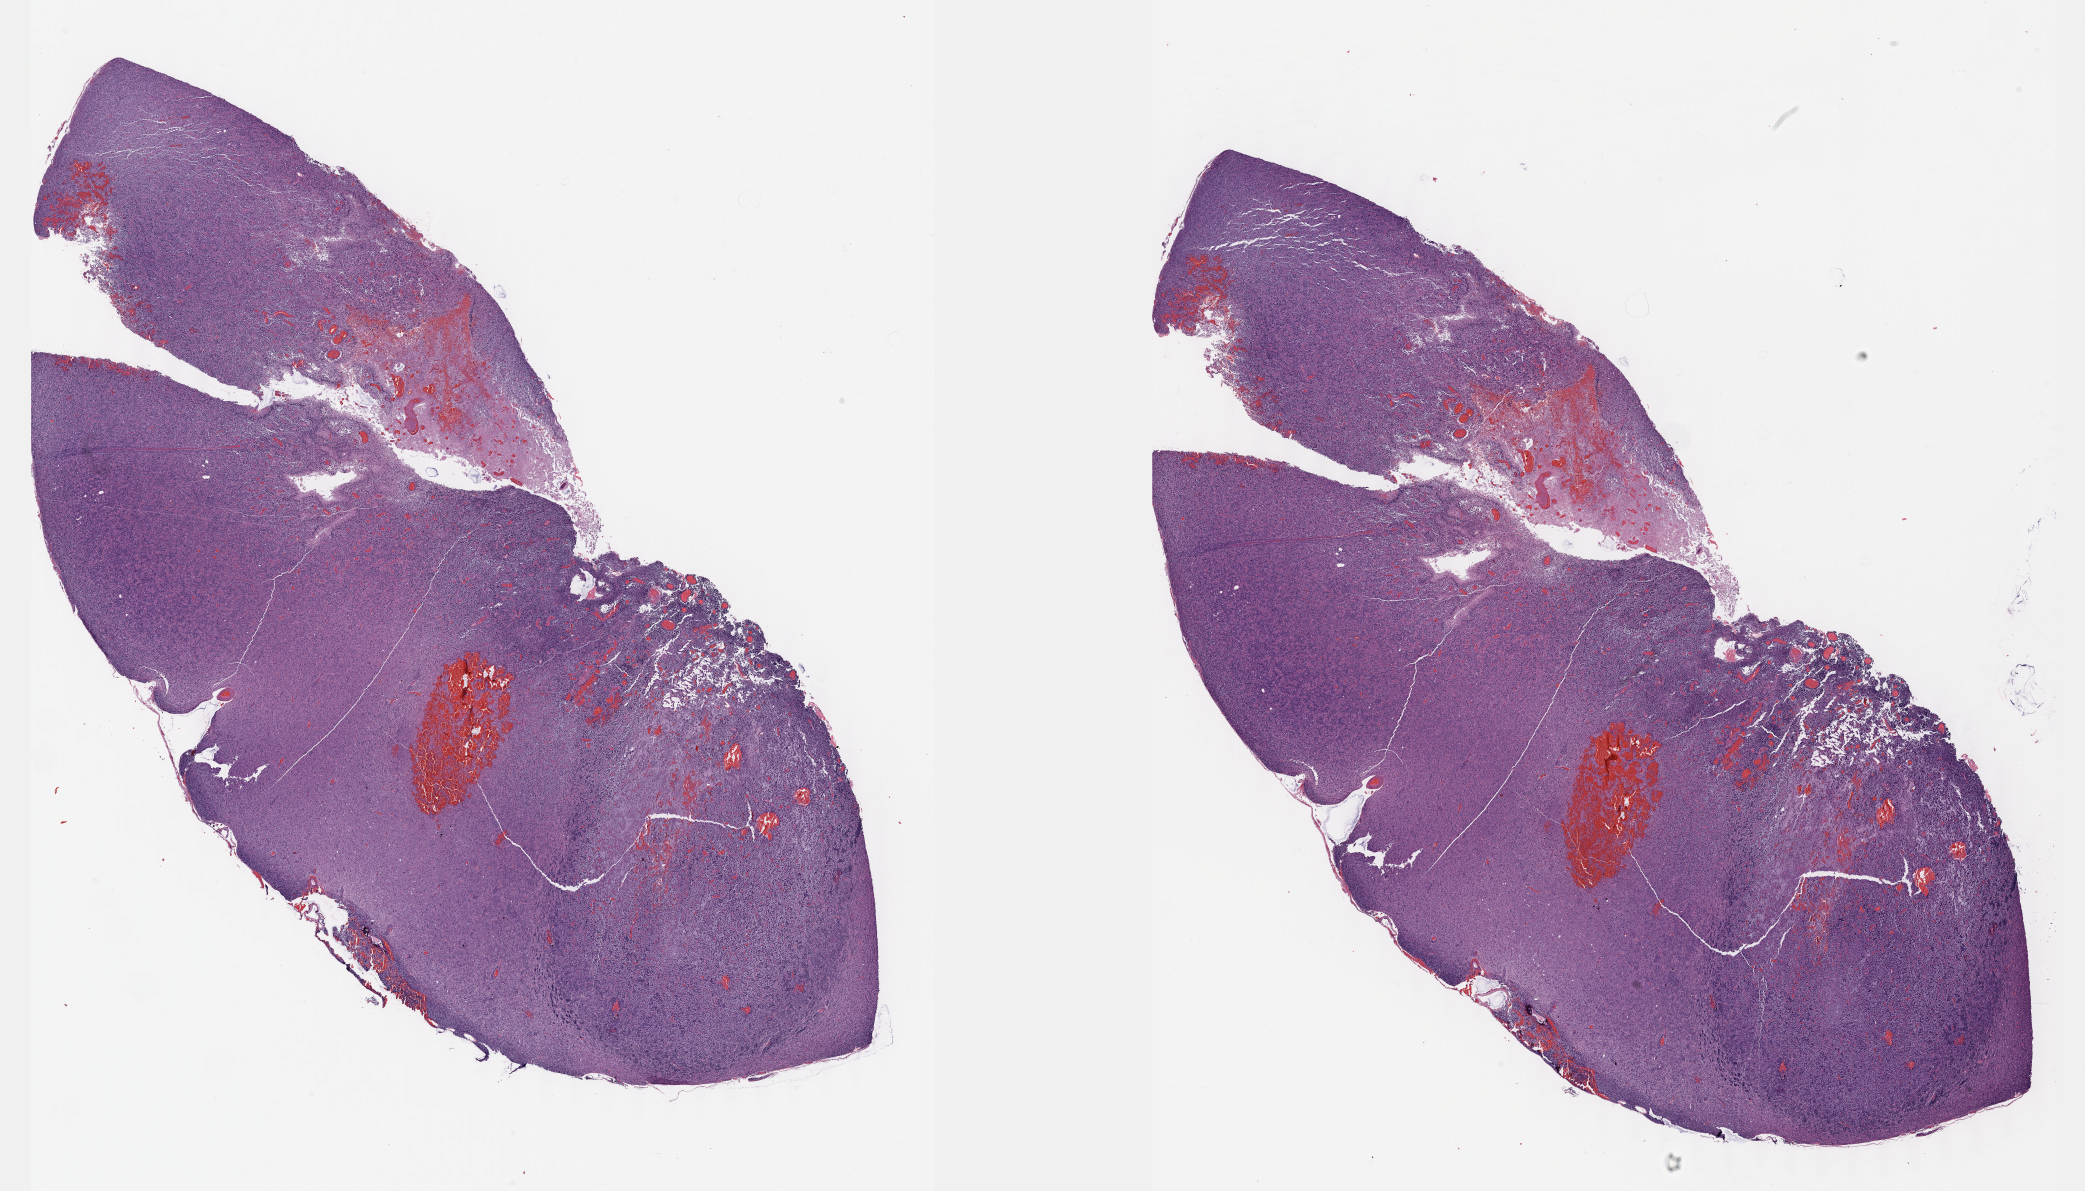
H&E whole-slide image — whole scanned area (about 33.7 x 19.3 mm, acquisition: 40x scan) shown as a low-resolution overview. Formalin-fixed paraffin-embedded (FFPE) diagnostic section. Primary tumour sample from the brain. Male patient; age at initial diagnosis 40 years.
Histologic diagnosis: Glioblastoma.